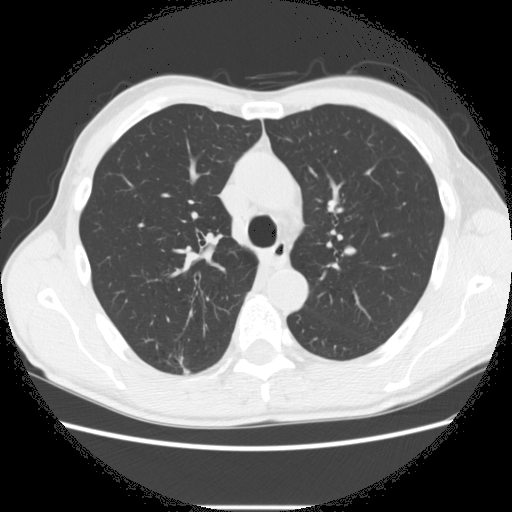
Low-dose screening chest CT, axial slice; second annual screen; lung window (W 1500 / L -600 HU); standard (soft-tissue) reconstruction kernel (STANDARD). Male participant, aged 66 years at enrolment. Former smoker at enrolment.
Expert-annotated lung lesion, bounding box [x1, y1, x2, y2] px = [165, 343, 220, 387]. The screening reader recorded 5 non-calcified nodules or masses ≥4 mm on this exam (right lower lobe, right upper lobe, right upper lobe, right upper lobe, left lower lobe); which of them this box marks is not recorded. Later outcome: lung cancer diagnosed 75 days after this screen — adenocarcinoma, NOS, right upper lobe, undifferentiated (G4), stage IA (AJCC 6th edition), 20 mm at pathology.